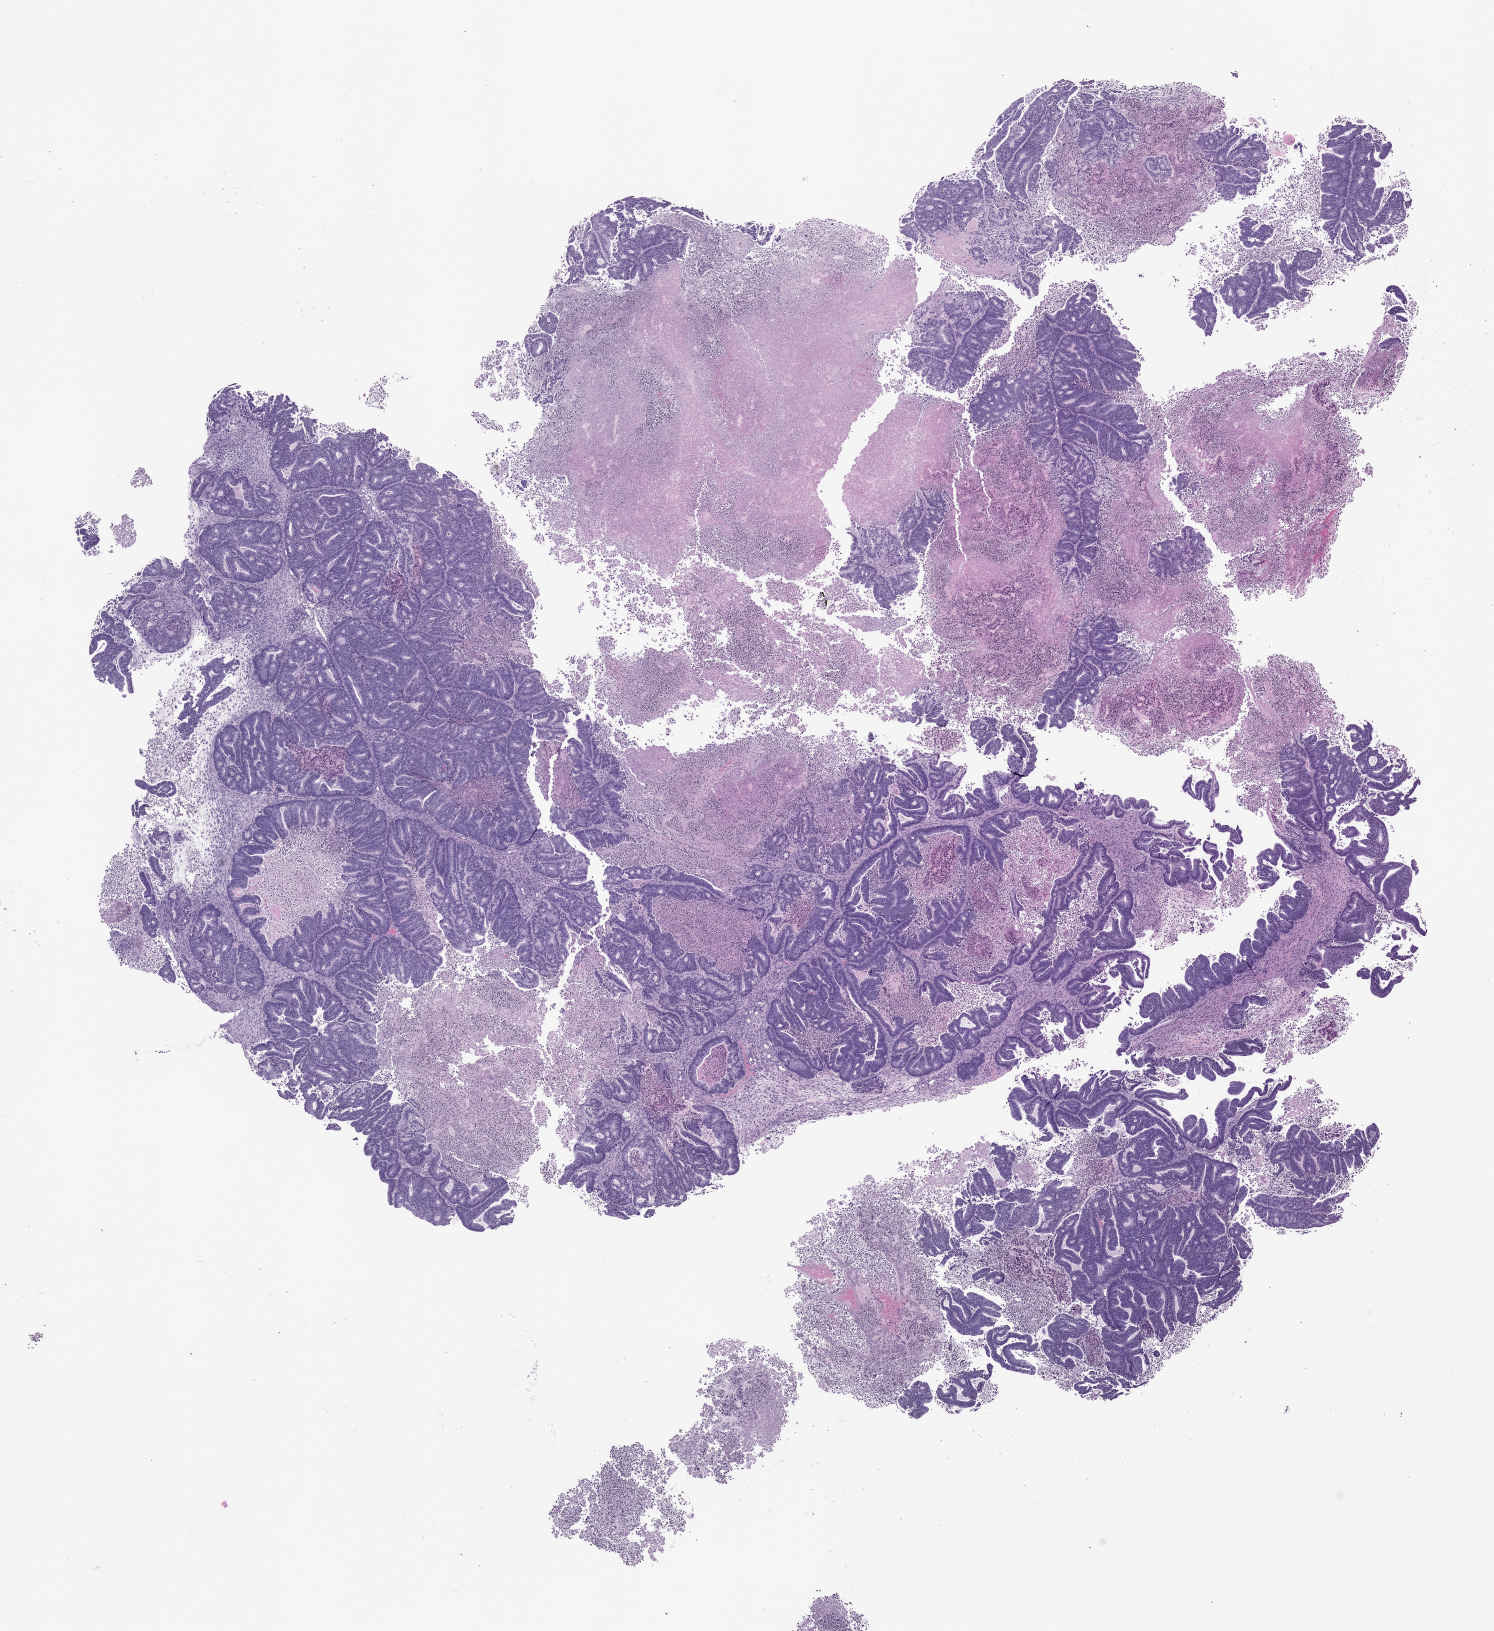
H&E whole-slide image of a patient-derived xenograft (PDX) tumor grown in a mouse, passage 0, low-resolution overview of the scanned area, about 12.0 x 13.1 mm, formalin-fixed, paraffin-embedded (FFPE) tissue, originating tumor site category: colon.
Originating patient diagnosis: Colon Adenocarcinoma.